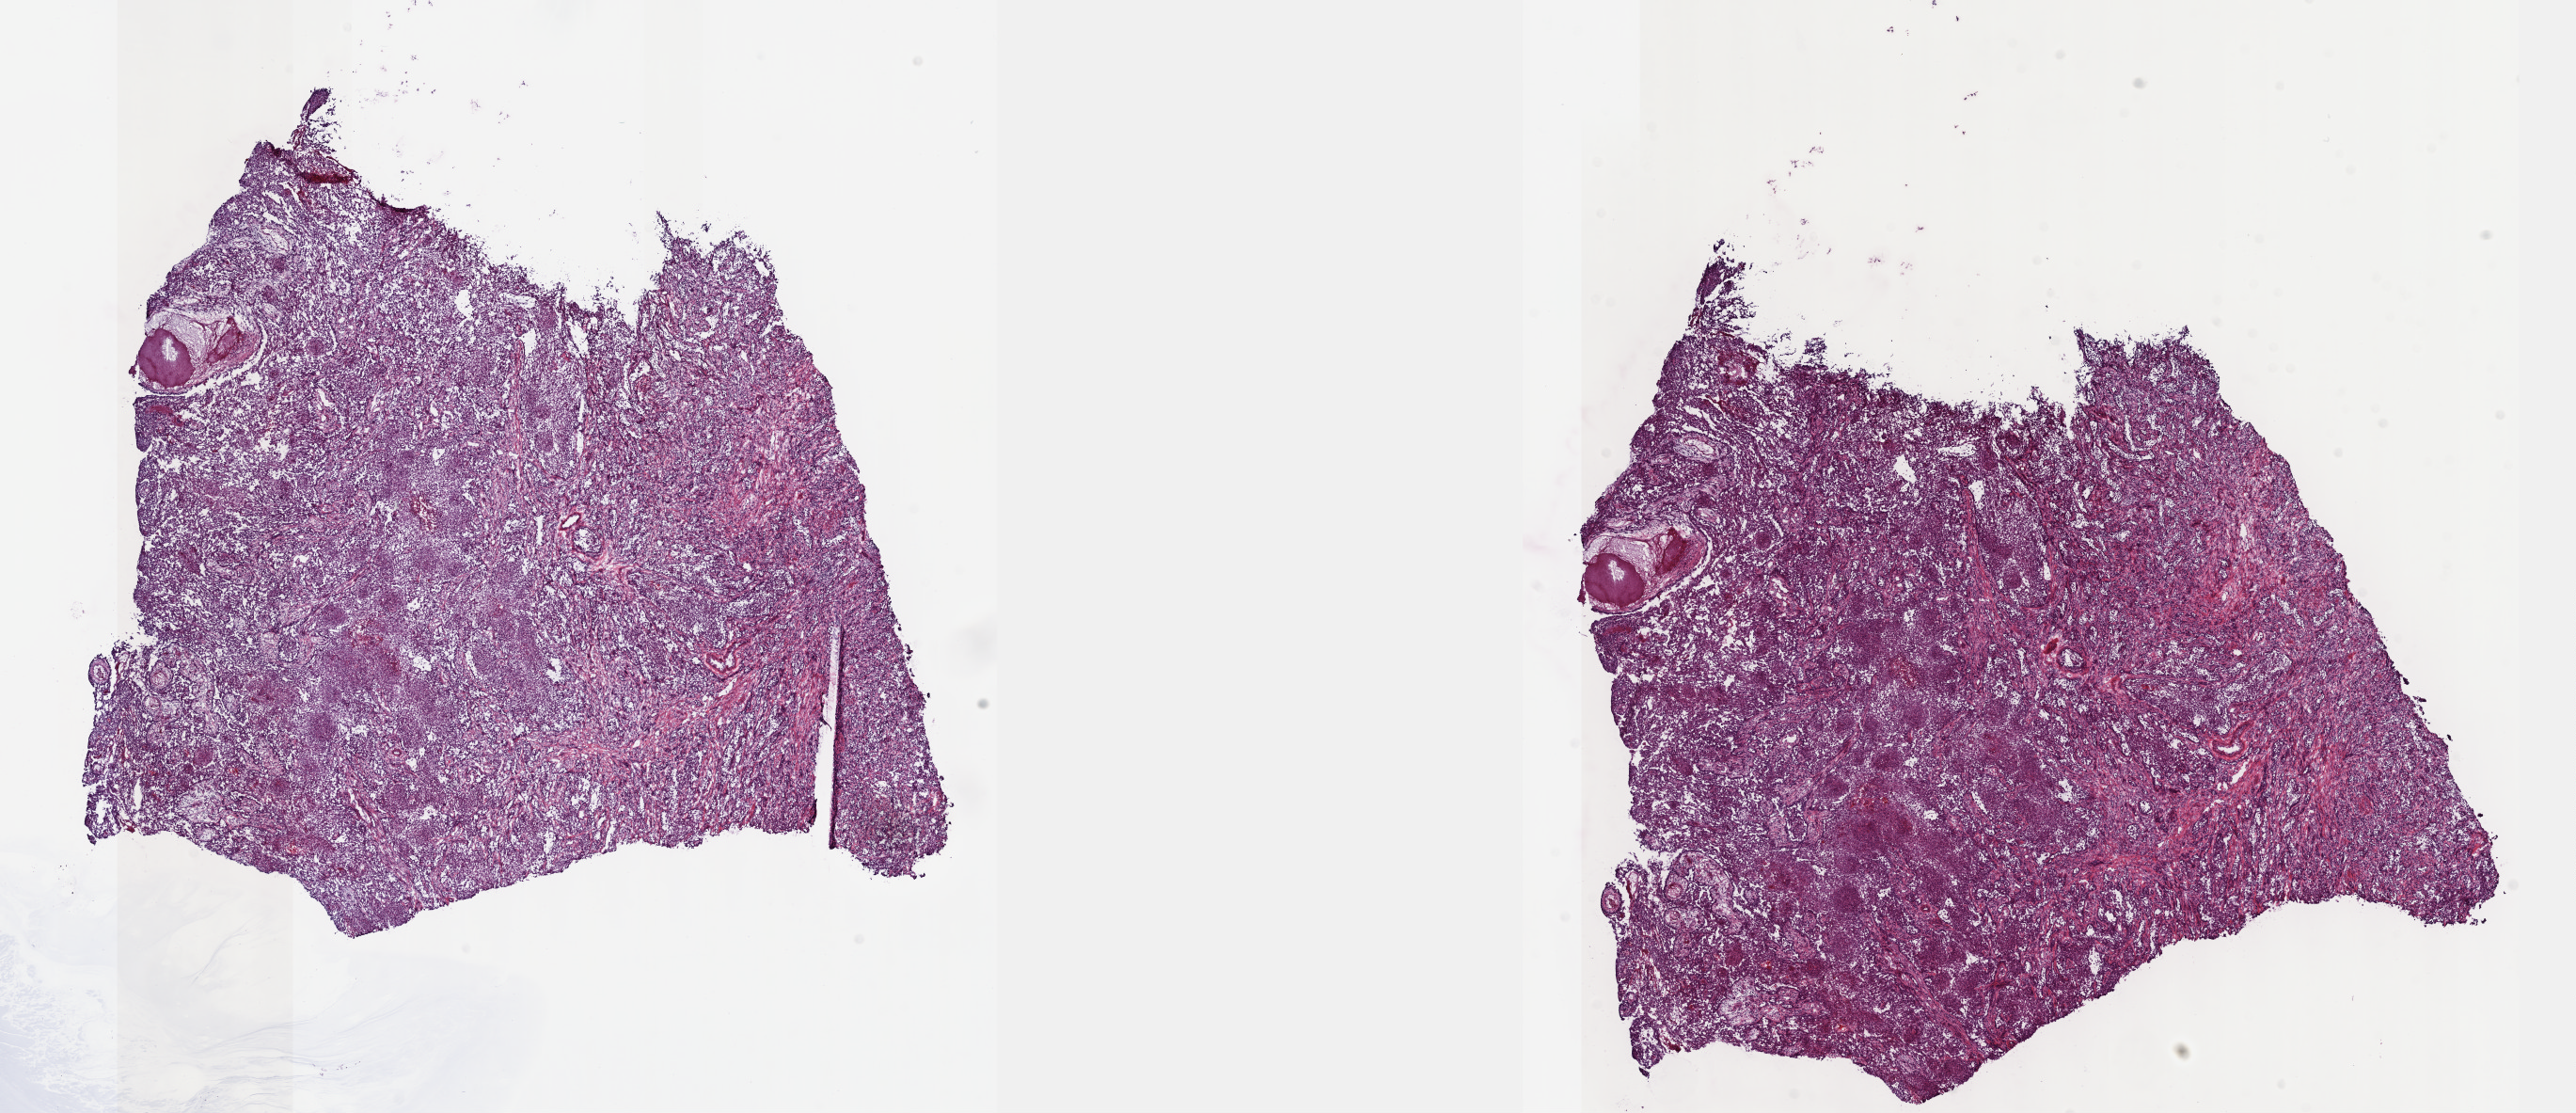
Whole-slide histology image, H&E-stained, whole scanned area (about 22.1 x 9.6 mm) shown as a low-resolution overview, frozen section, sample: primary tumour, bladder. Male, age 48 years at initial diagnosis. Histologic grade: high grade. Slide review estimates, as recorded: tumour cells 80%, tumour nuclei 90%, normal cells 0%, stromal cells 20%, necrosis 0%. Infiltration values recorded for this section: lymphocyte infiltration 0%, monocyte infiltration 0%, neutrophil infiltration 0%.
* histologic diagnosis: Transitional cell carcinoma
* lymph nodes positive (case pathology): 1 of 61 examined
* AJCC pathologic stage: IV (6th edition)